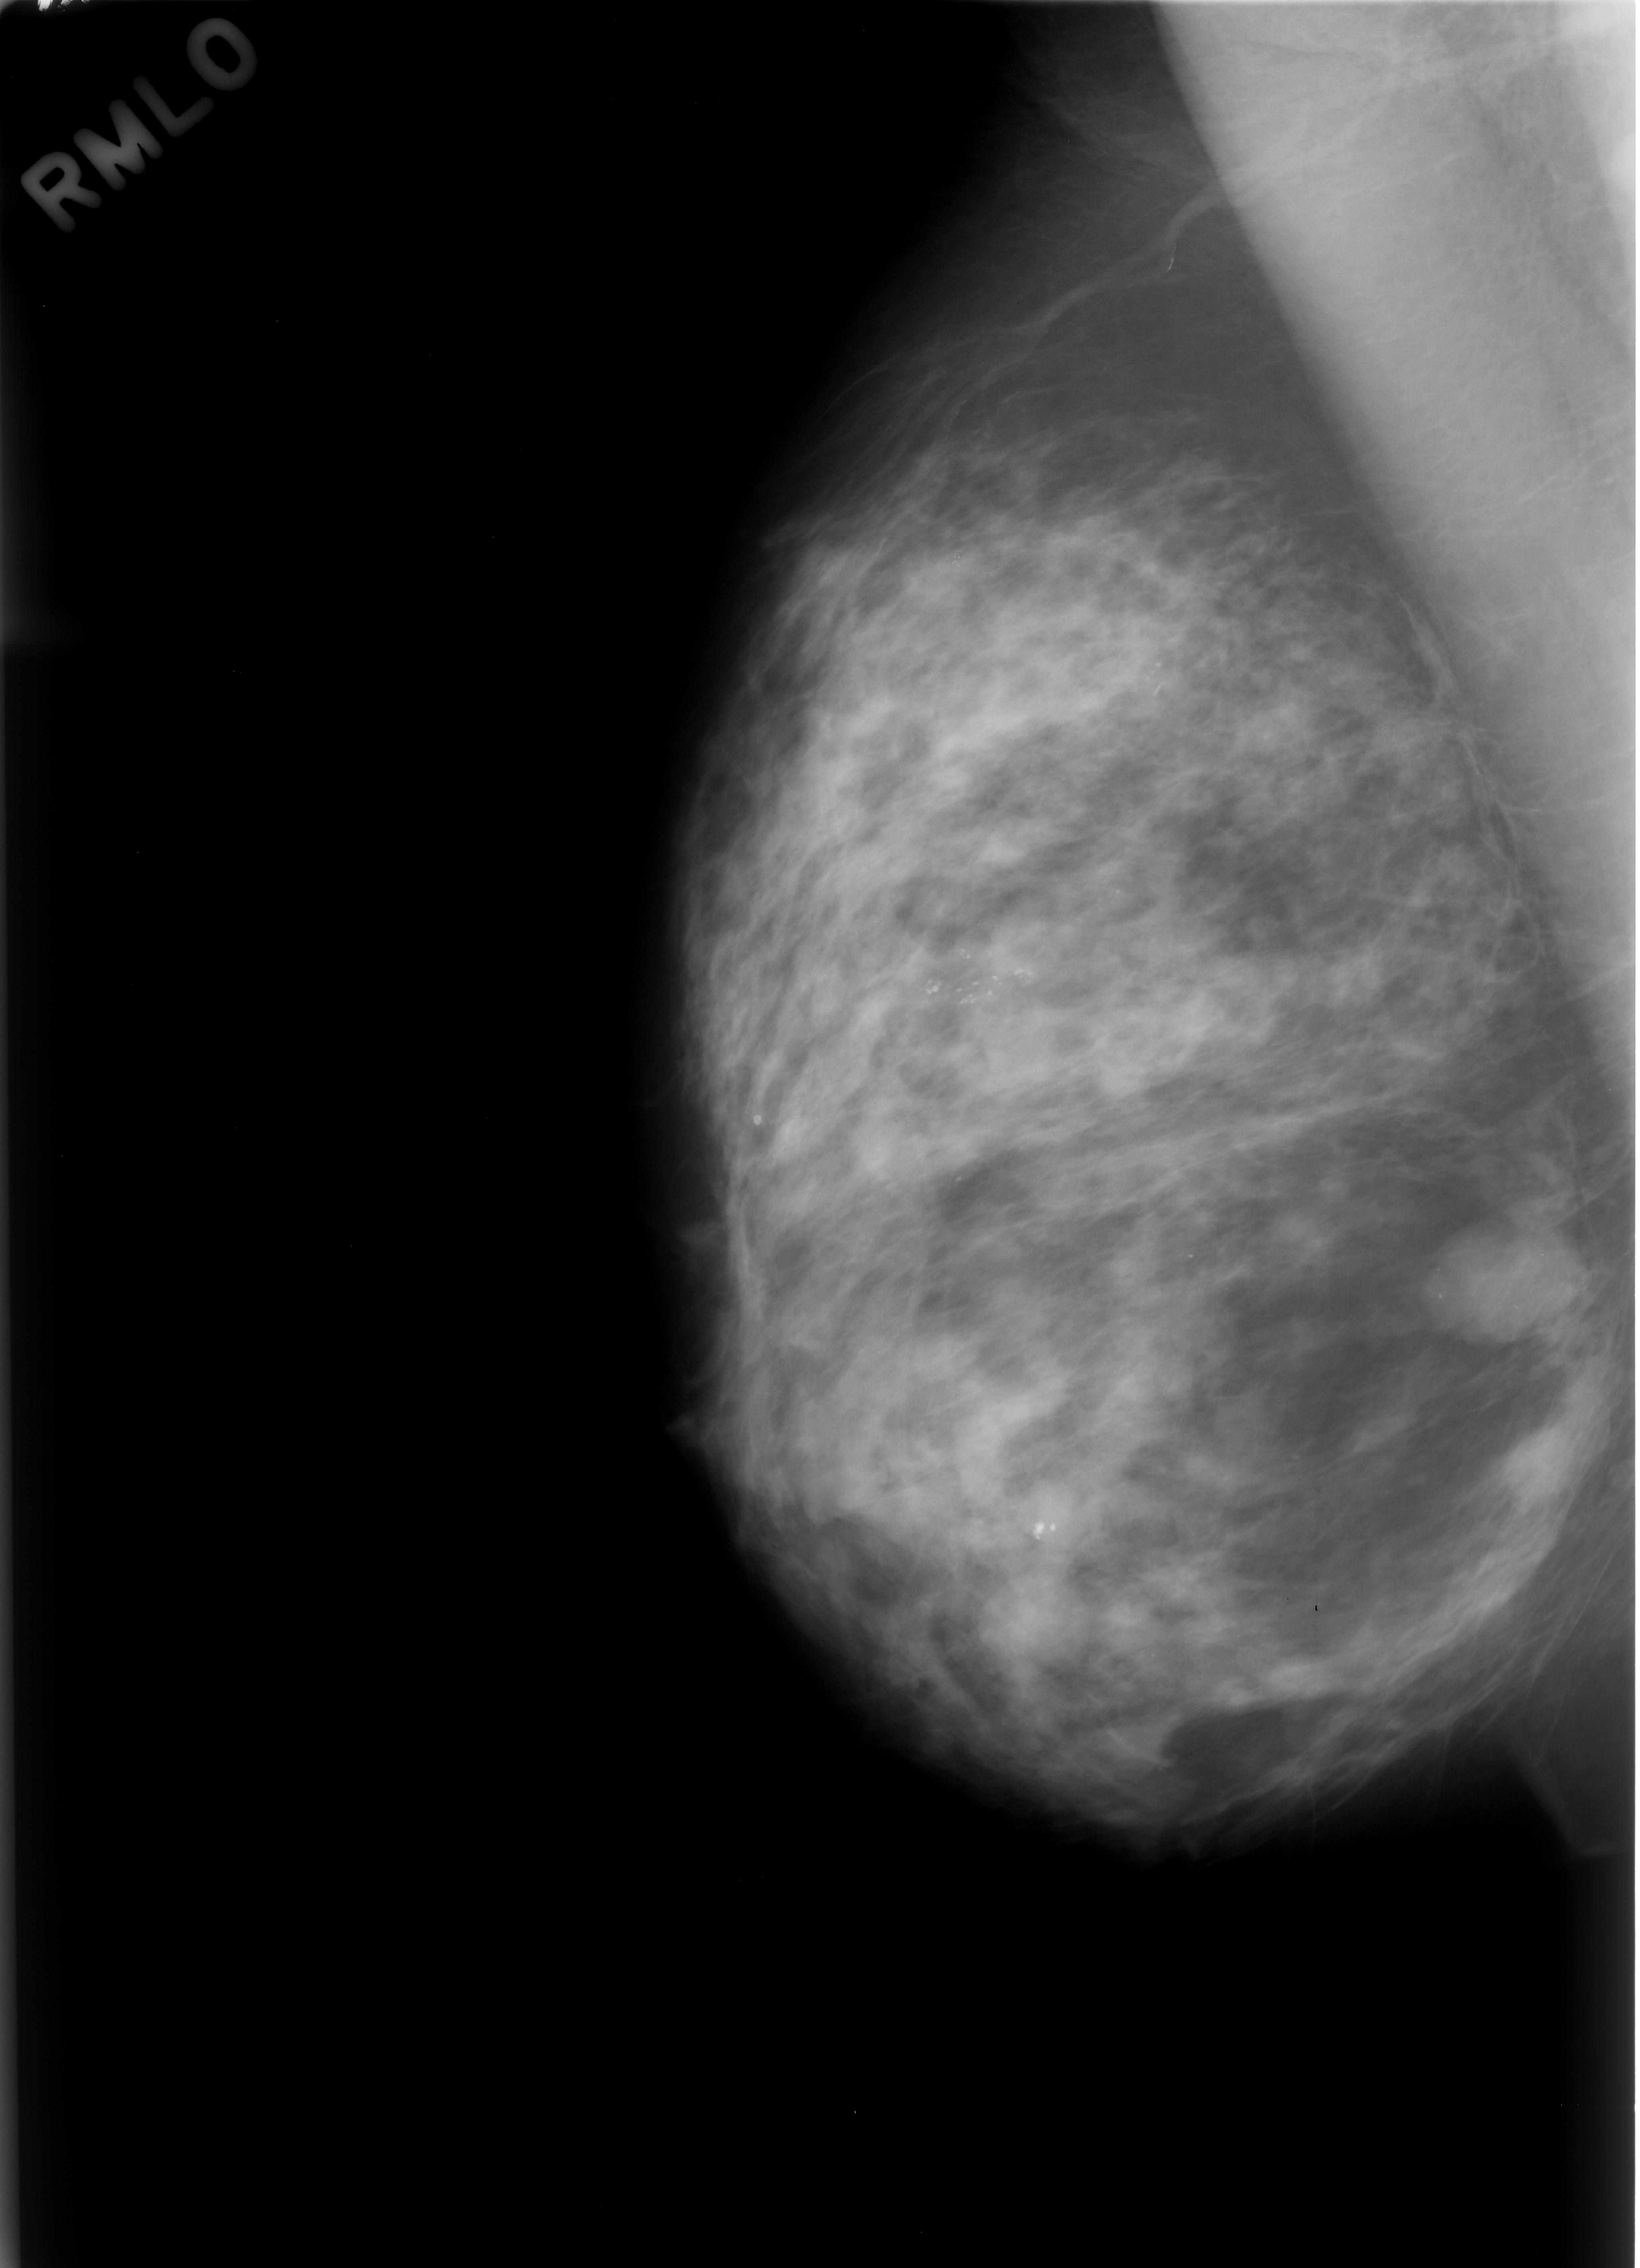
Mammogram (digitized film); right breast; mediolateral oblique (MLO) view; breast composition: heterogeneously dense (BI-RADS density category 3 of 4).
Abnormality record for this image: Finding 1 of 2: calcifications, morphology pleomorphic, distribution clustered; BI-RADS assessment category 4; pathology (as recorded): benign. Finding 2 of 2: calcifications, morphology pleomorphic, distribution clustered; BI-RADS assessment category 4; subtlety rating 4 on a 1 (subtle) to 5 (obvious) scale; pathology result (as recorded, not read from the image): benign.